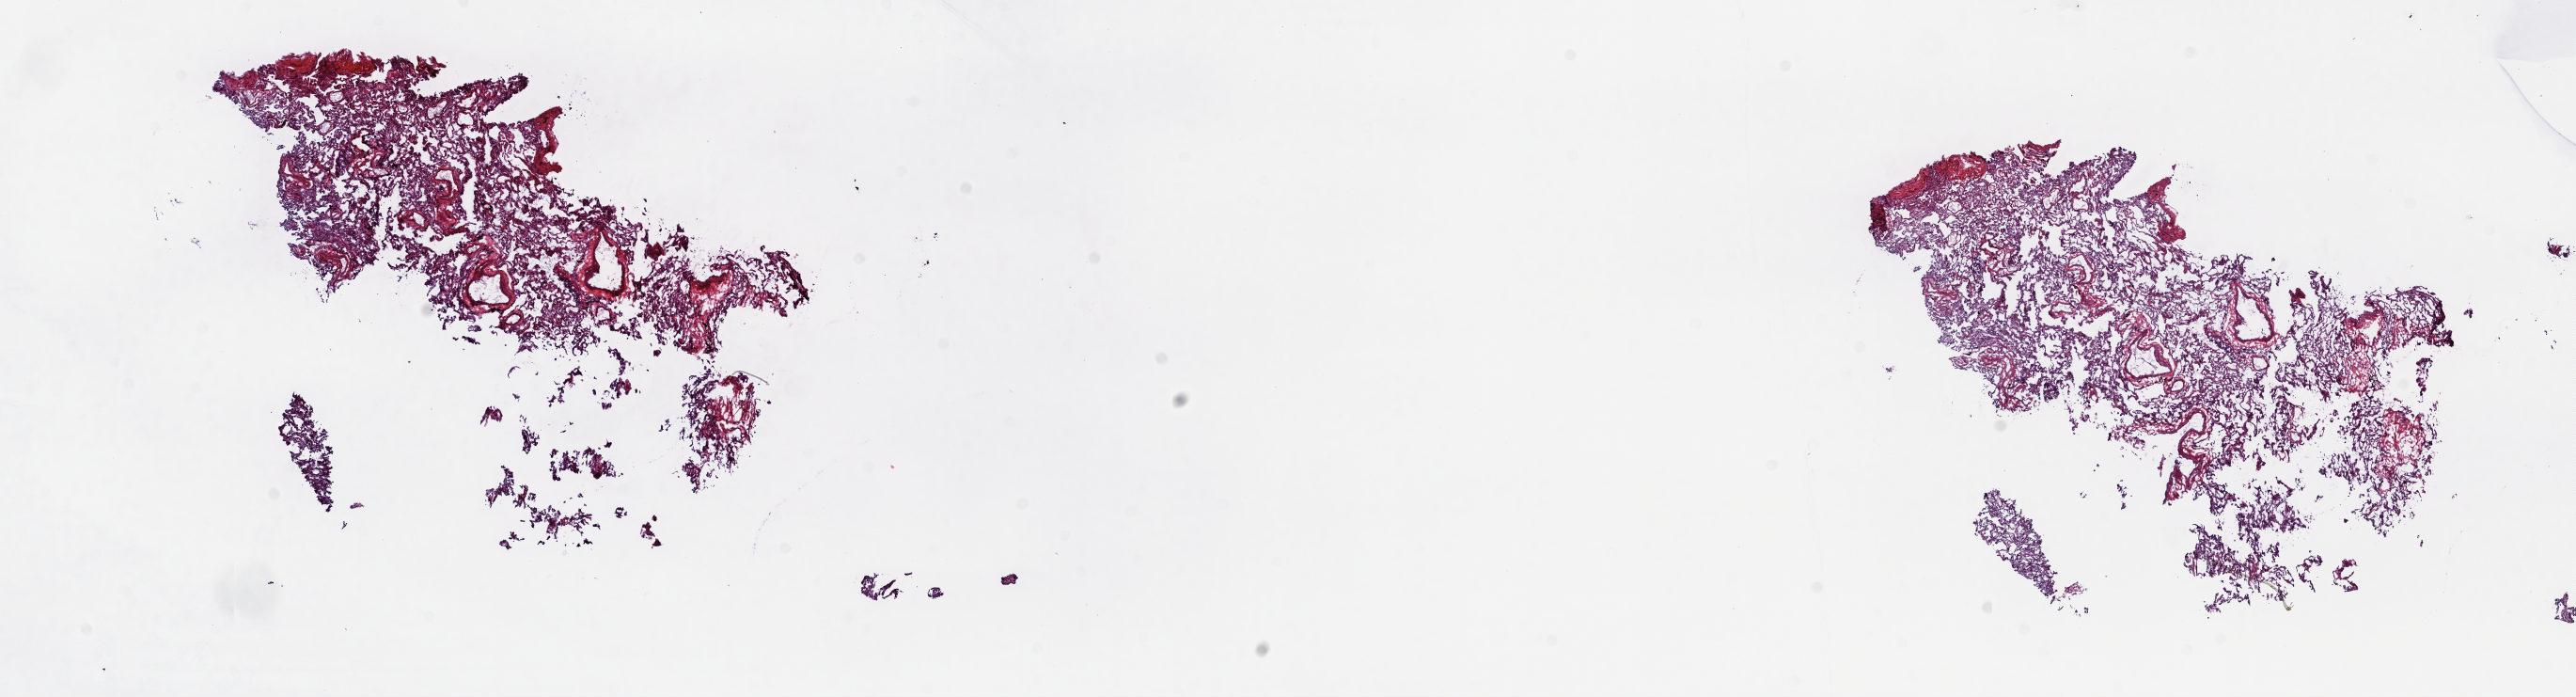
Digitized H&E tissue section (whole slide), shown as a low-resolution overview of the whole scanned area (about 22.1 x 6.0 mm). Frozen section from the top of the tissue portion. Lung, solid tissue normal (non-tumour tissue) sample. Patient: male, age at initial diagnosis 68 years. Slide review estimates, as recorded: tumour cells 0%, tumour nuclei 0%, normal cells 50%, stromal cells 50%, necrosis 0%. Inflammatory infiltration, as recorded: lymphocyte infiltration 3%, monocyte infiltration 7%, neutrophil infiltration 2%.
- this section: solid tissue normal sample (biorepository sample class)
- patient diagnosis: Adenocarcinoma, NOS (upper lobe, lung)